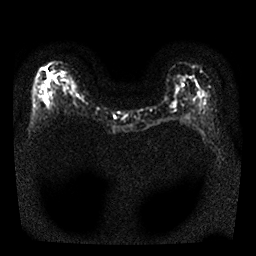
Breast MRI, one axial slice. Position 13 of 25 along the scan axis. Diffusion-weighted series; image 2 of 4 stored at this slice position (different b-values; order by instance number). 1.5 T. 4 mm slice thickness. 256 × 256 image matrix, field of view 300 × 300 mm. Female patient.
Annotated regions visible in this slice (outlined manually by an expert reader):
- tumour on diffusion-weighted imaging: box from (x=47, y=73) to (x=52, y=79) px